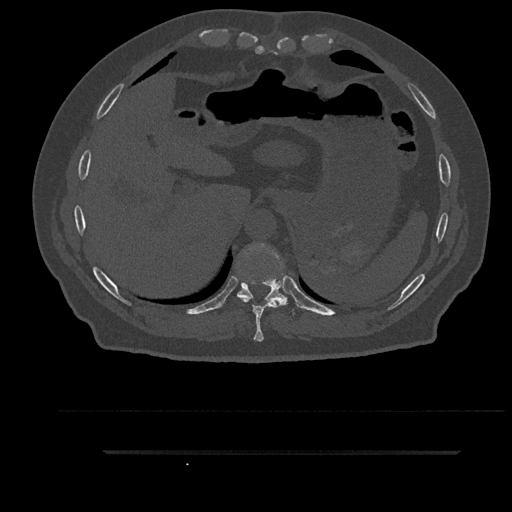
CT including the spine, one axial slice; position 393 of 797 along the scan axis; 120 kVp; bone window (W 1800 / L 400 HU); 512 × 512 image matrix, field of view 432 × 432 mm. Male patient, age 63 years. From the clinical record (not read from this slice): primary cancer: renal; vertebrae with lytic lesions (as recorded): T8.
Outlined on this slice (semi-automatic segmentation, software-assisted and operator-edited):
- T10 vertebra: bounding box [x1, y1, x2, y2] px = [236, 243, 300, 315]
- T9 vertebra: [238, 279, 288, 342]